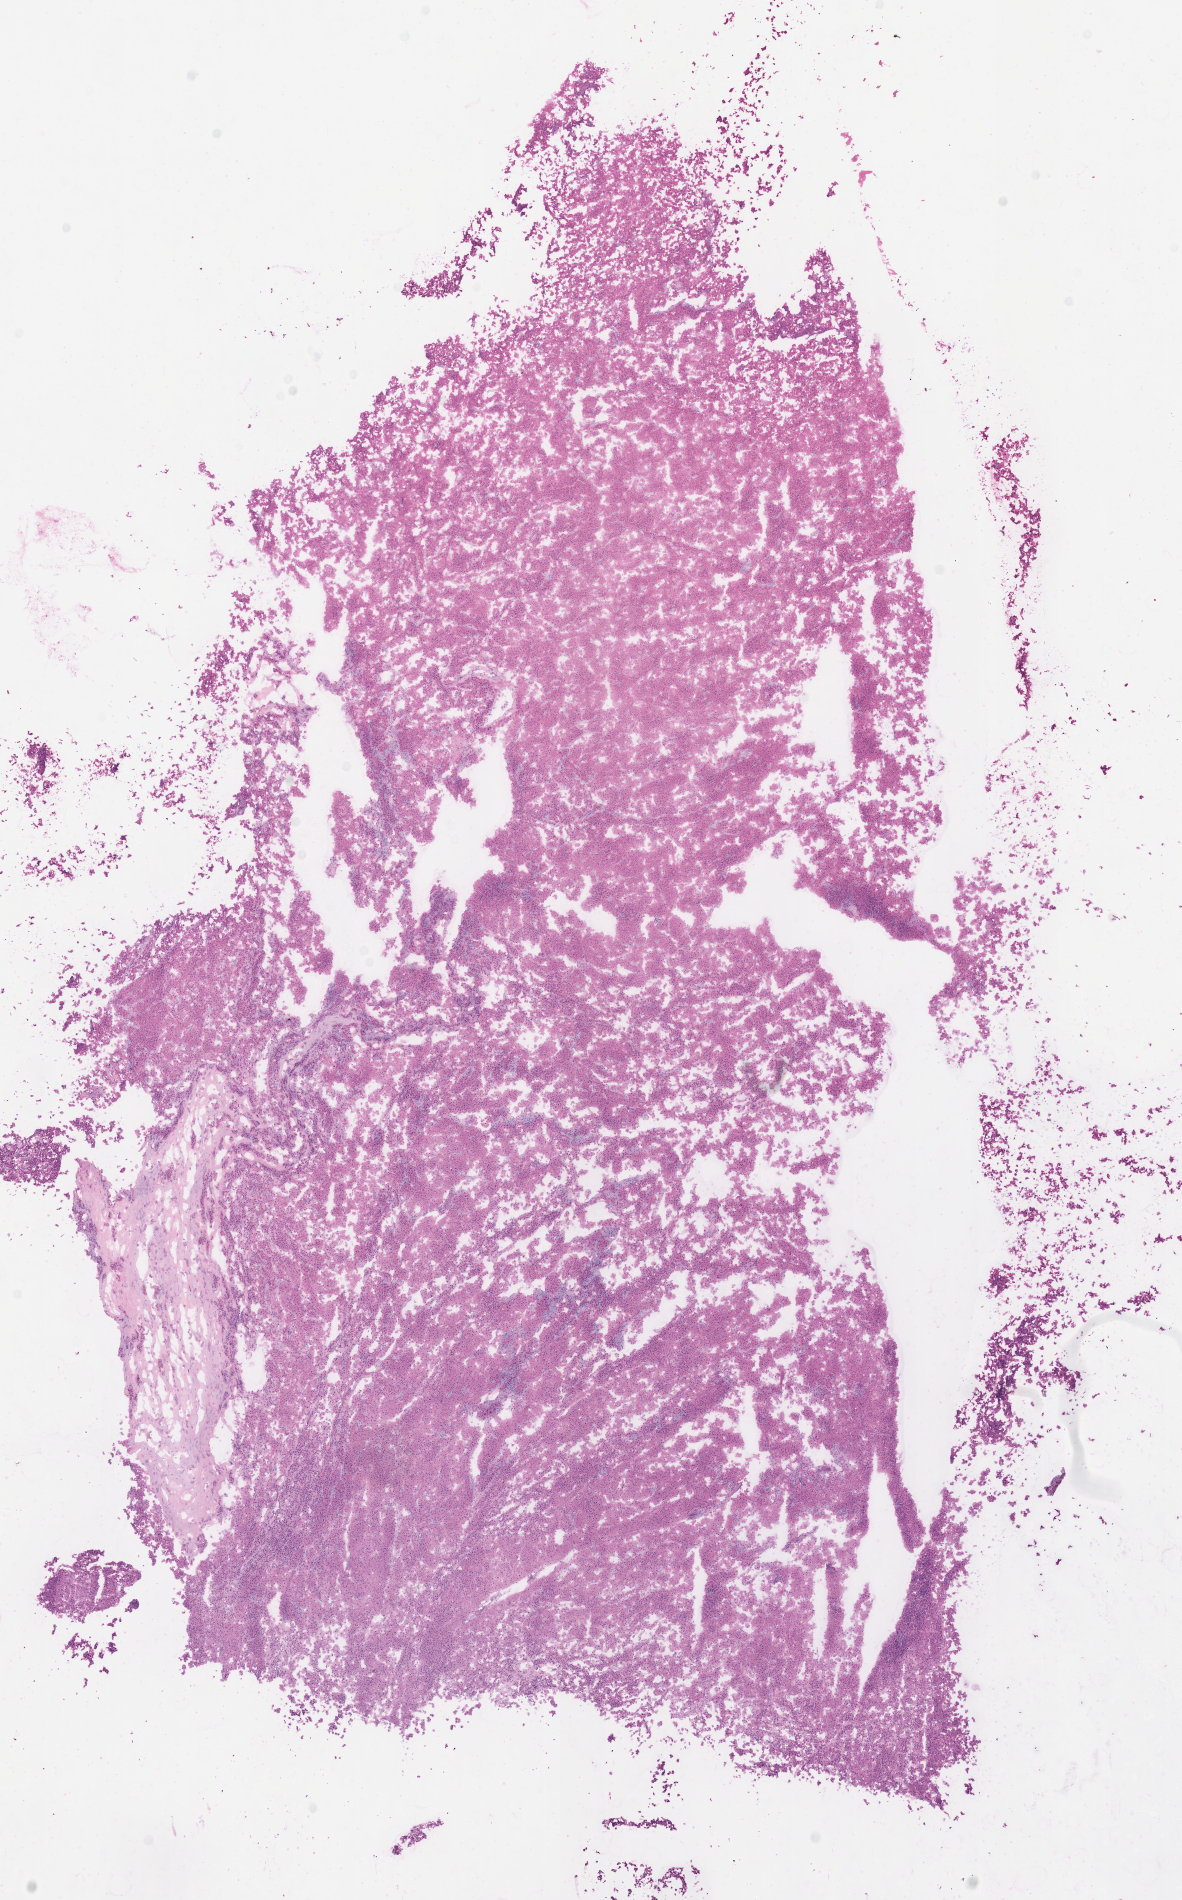
Whole-slide histology image, H&E-stained, shown as a low-resolution overview of the whole scanned area (about 9.3 x 14.9 mm, acquisition: 40x scan); frozen section from the top of the tissue portion; sample: primary tumour, kidney. Female, age 45 years at initial diagnosis. Slide review estimates, as recorded: tumour cells 90%, tumour nuclei 85%, normal cells 0%, stromal cells 10%, necrosis 0%.
Lymph nodes positive (case pathology): 0 of 5 examined. AJCC pathologic stage: II (5th edition). Histologic diagnosis: Renal cell carcinoma, chromophobe type.